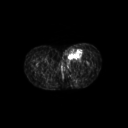
FDG PET of an extremity soft-tissue mass (from a PET/CT study), one axial slice; position 47 of 267 along the scan axis; 3.27 mm slice thickness; 128 × 128 image matrix, field of view 600 × 600 mm. Female patient, age 24 years. From the clinical record (not read from this slice): histological type: leiomyosarcoma; grade: high; site of the primary tumour: groin.
Outlined on this slice (expert contour drawn on MRI and transferred to this co-registered scan by the dataset authors):
- gross tumour volume including surrounding oedema: bounding box <62,46,82,63> (left, top, right, bottom; pixels)
- gross tumour volume (mass): <67,49,82,58>